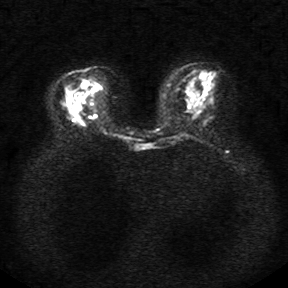
Breast MRI, one axial slice; slice 10 of 34 in the series (ordered by position); diffusion-weighted series; image 2 of 4 stored at this slice position (different b-values; order by instance number); 1.5 T; 288 × 288 image matrix, field of view 340 × 340 mm. Female patient.
Annotated regions visible in this slice (outlined manually by an expert reader):
- tumour on diffusion-weighted imaging: box from (x=82, y=81) to (x=88, y=88) px